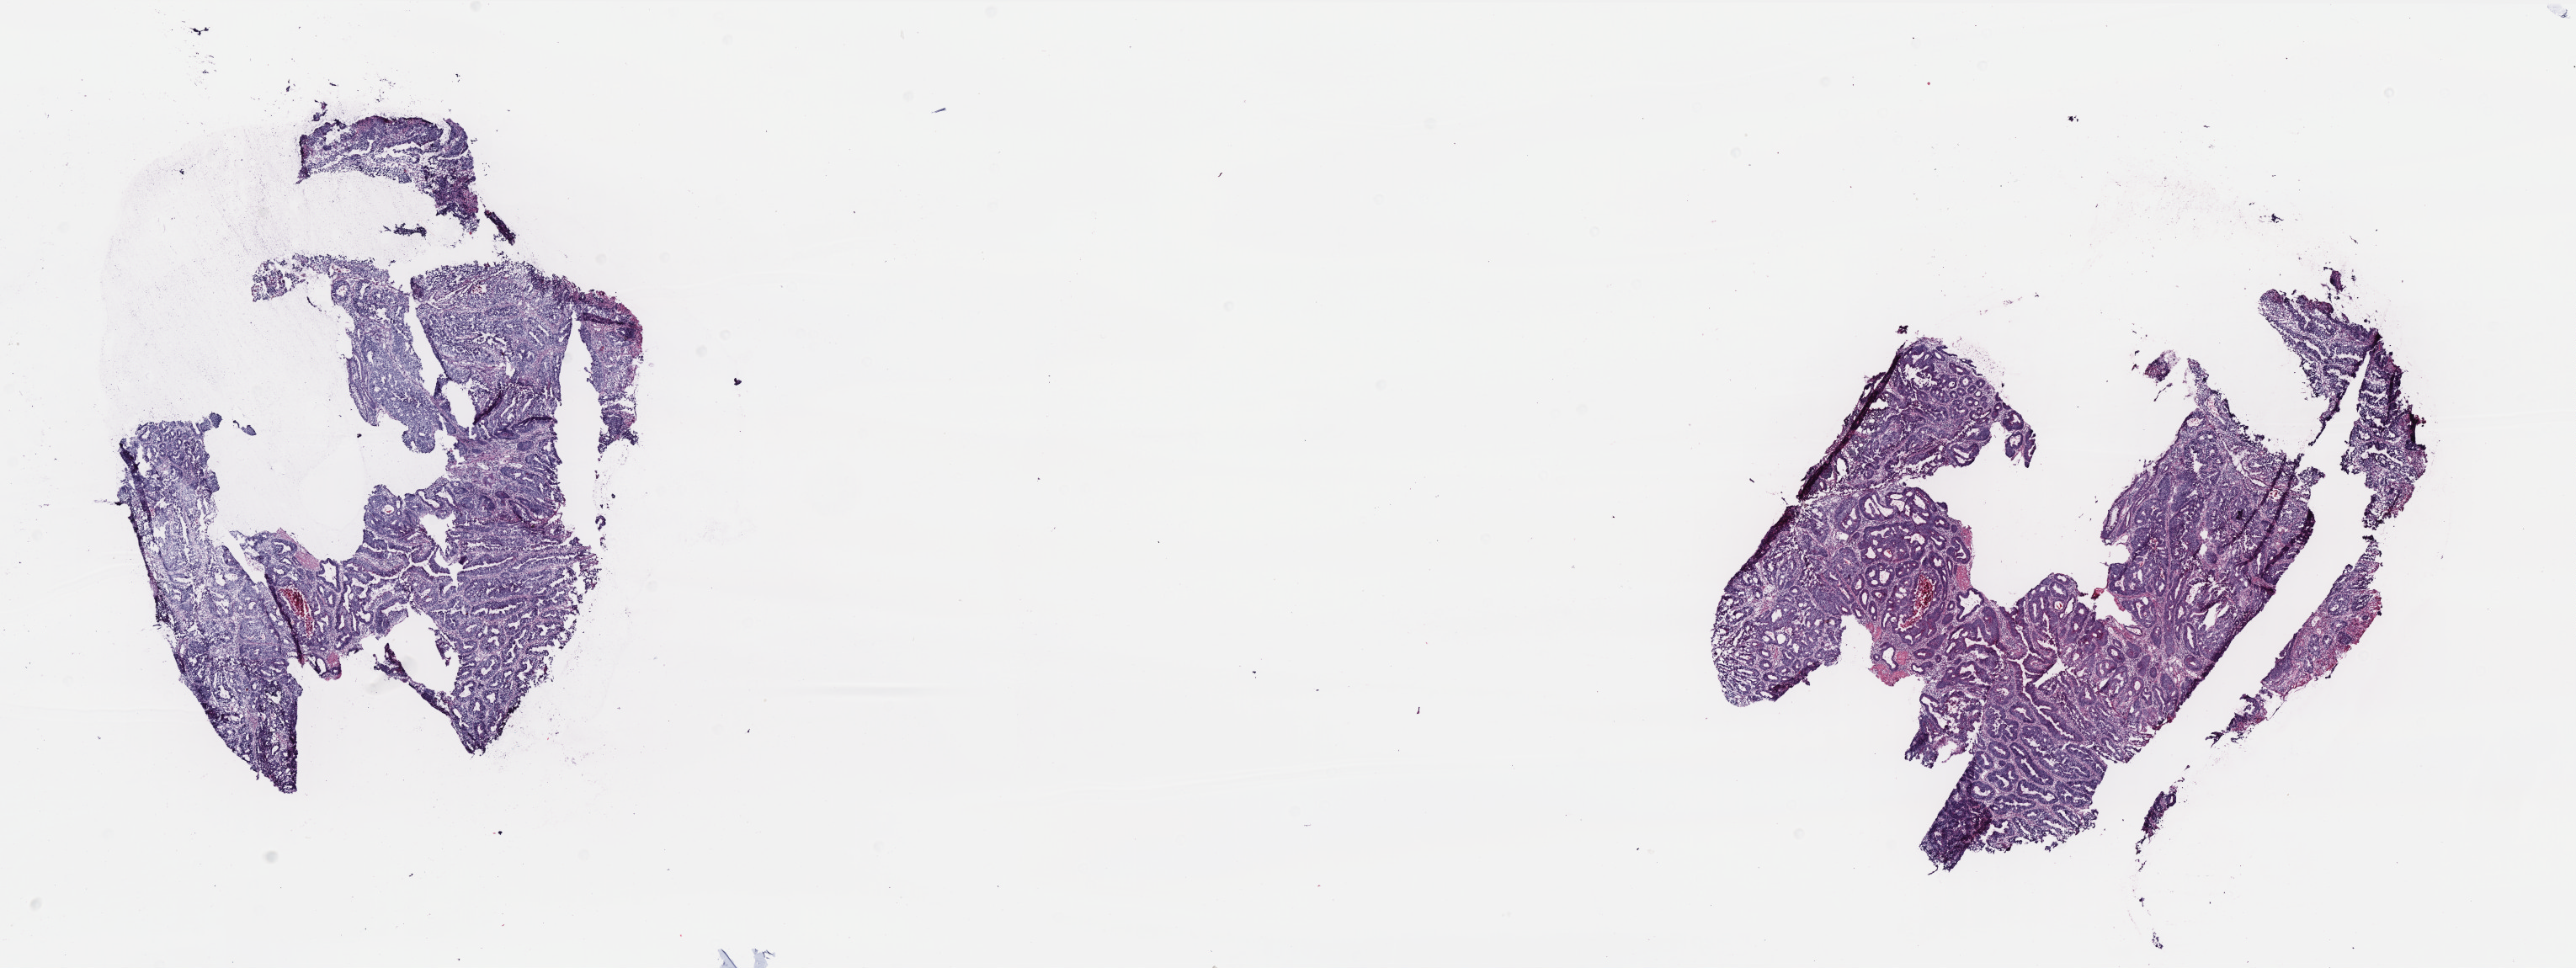
Digitized Hematoxylin and eosin (H&E) stained tissue section (whole slide) — whole scanned area (about 24.5 x 9.2 mm) shown as a low-resolution overview. Frozen section from the bottom of the tissue portion. Colon, primary tumour sample. Female, age 74 years at initial diagnosis. Slide review estimates, as recorded: tumour cells 80%, tumour nuclei 80%, normal cells 2%, stromal cells 15%, necrosis 3%. Inflammatory infiltration, as recorded: lymphocyte infiltration 5%, monocyte infiltration 1%, neutrophil infiltration 1%.
* TNM: T3 N2 M1
* AJCC pathologic stage: IV (6th edition)
* lymph nodes positive (case pathology): 6 of 12 examined
* histologic diagnosis: Adenocarcinoma, NOS (sigmoid colon)